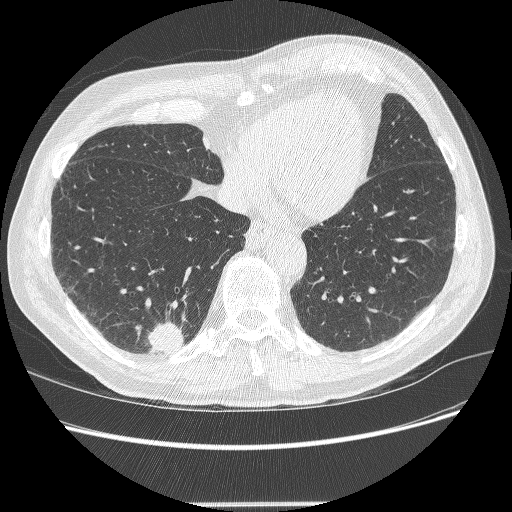
Axial slice from a low-dose chest CT screening exam; second annual screen; lung window (W 1500 / L -600 HU); 512 × 512 image matrix. Male, age 71 years at enrolment.
- Expert reader's lesion annotation, box from (x=137, y=322) to (x=188, y=362) px.
- The screening reader recorded 5 non-calcified nodules or masses ≥4 mm on this exam (right lower lobe, right lower lobe, right upper lobe, right upper lobe, right upper lobe); which of them this box marks is not recorded.
- Official screen result: positive, change unspecified: nodule(s) >= 4 mm or enlarging nodule(s), mass(es), or other non-specific abnormalities suspicious for lung cancer.
- Later outcome: lung cancer diagnosed 7 days after this screen — squamous cell carcinoma, NOS, right lower lobe, moderately differentiated (G2), stage IA (AJCC 6th edition), 27 mm at pathology.